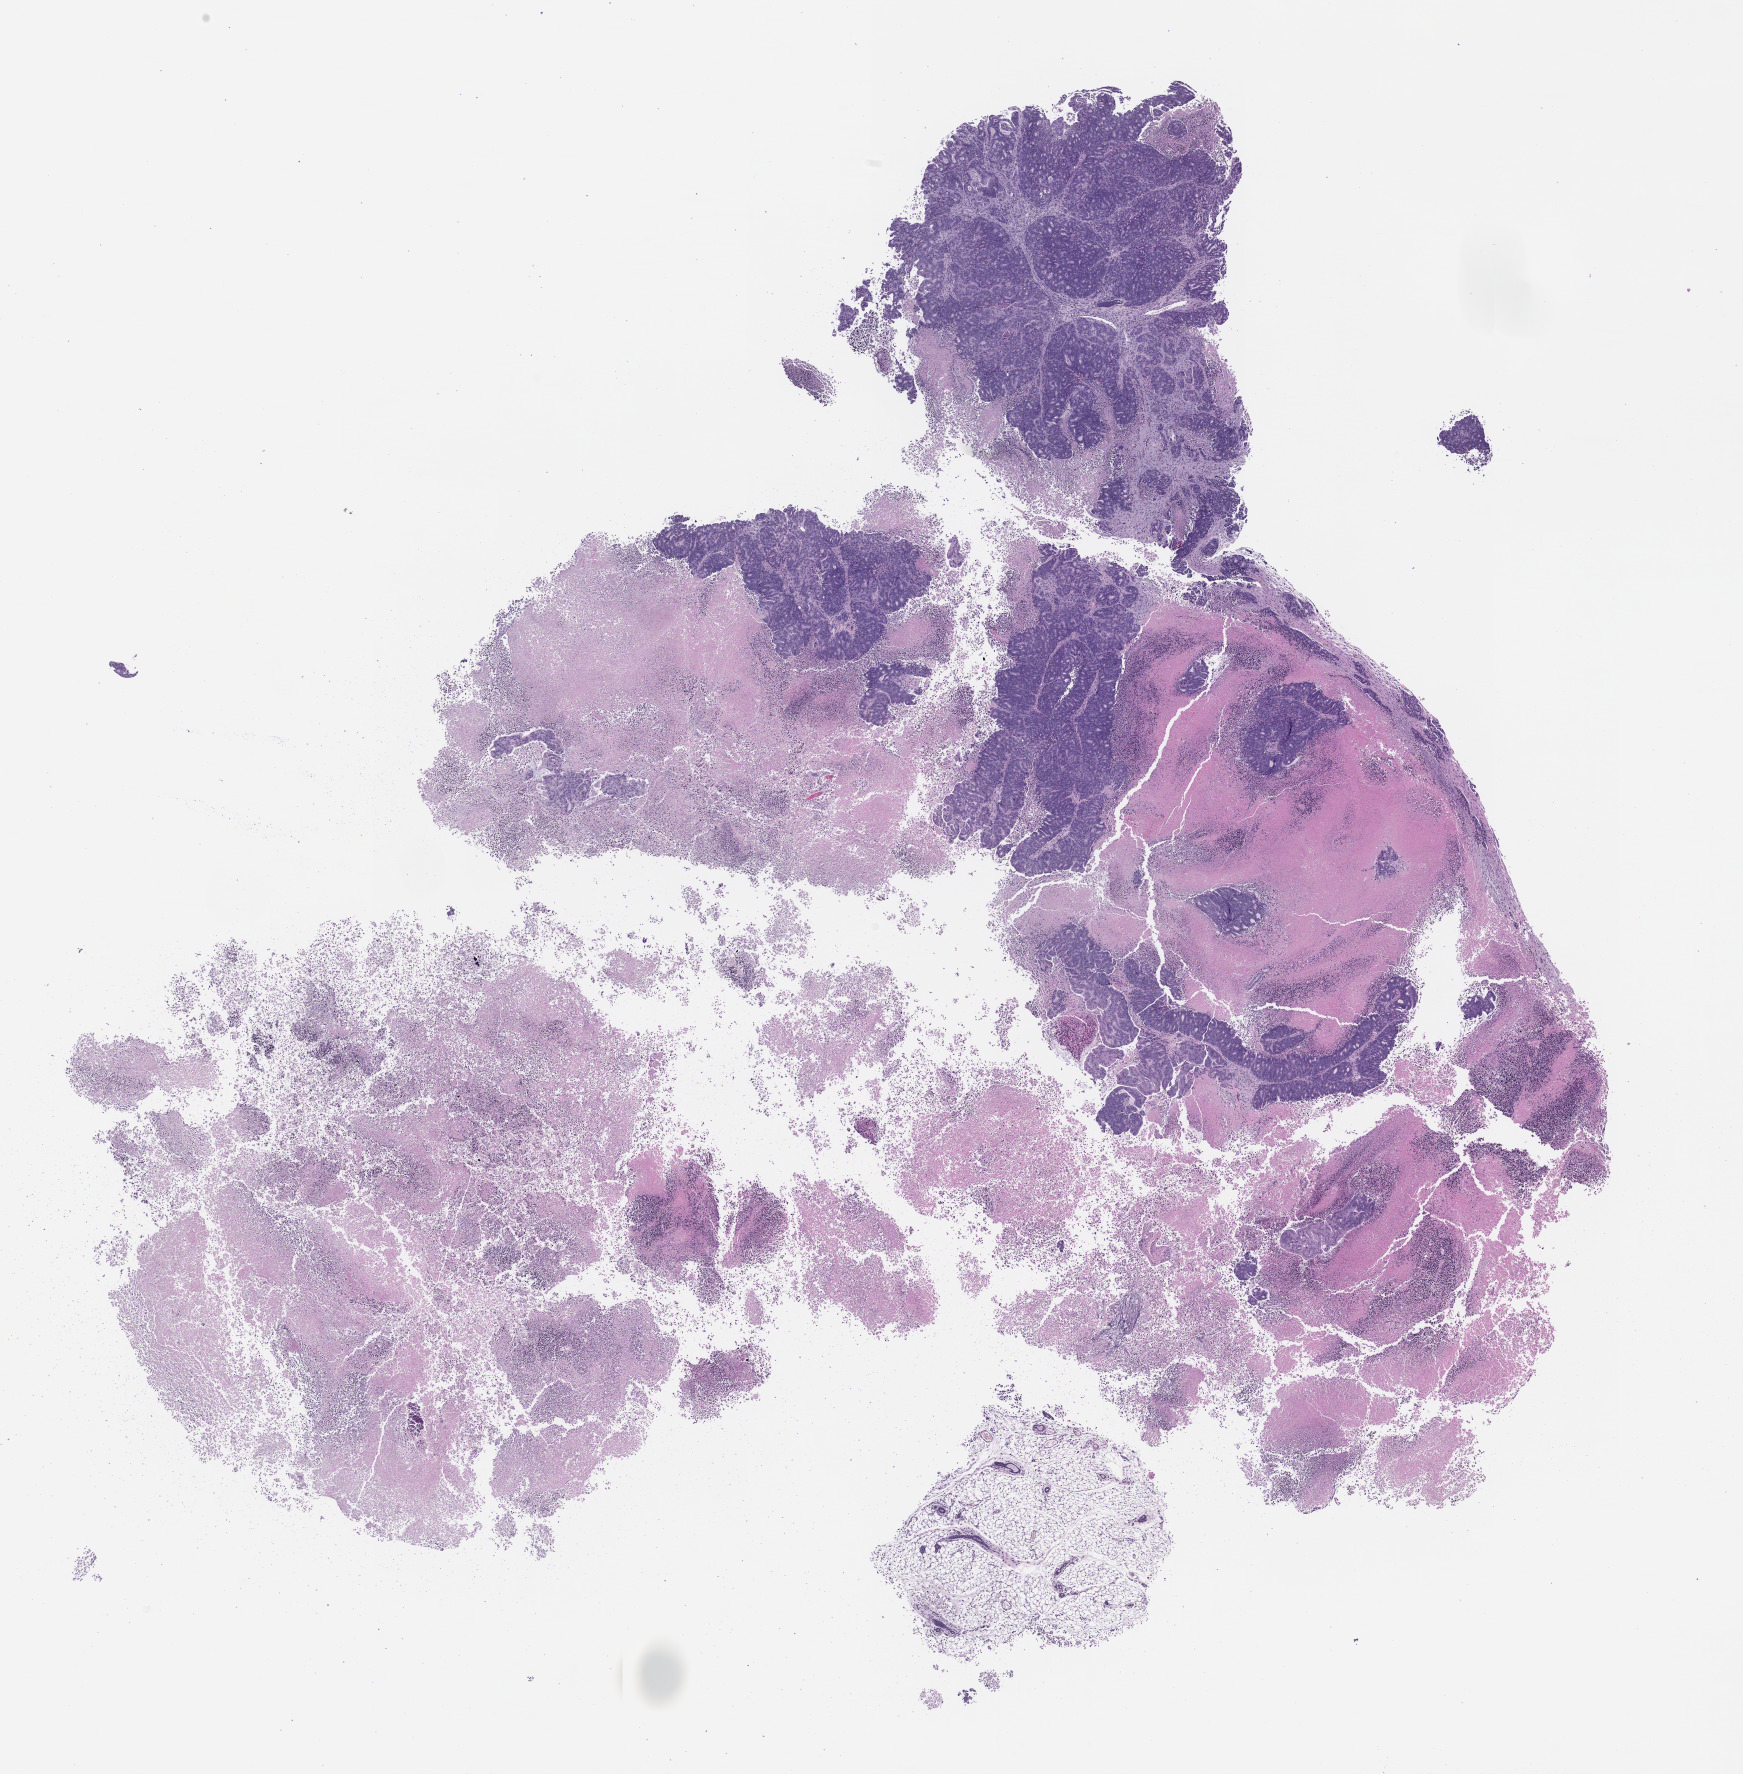
Haematoxylin and eosin whole-slide image of a patient-derived xenograft (PDX) tumor grown in a mouse, passage 0, a low-resolution overview of the entire scanned area, about 14.0 x 14.3 mm; formalin-fixed, paraffin-embedded (FFPE) tissue; tumor site category: colon.
Originating patient diagnosis: Colon Adenocarcinoma.